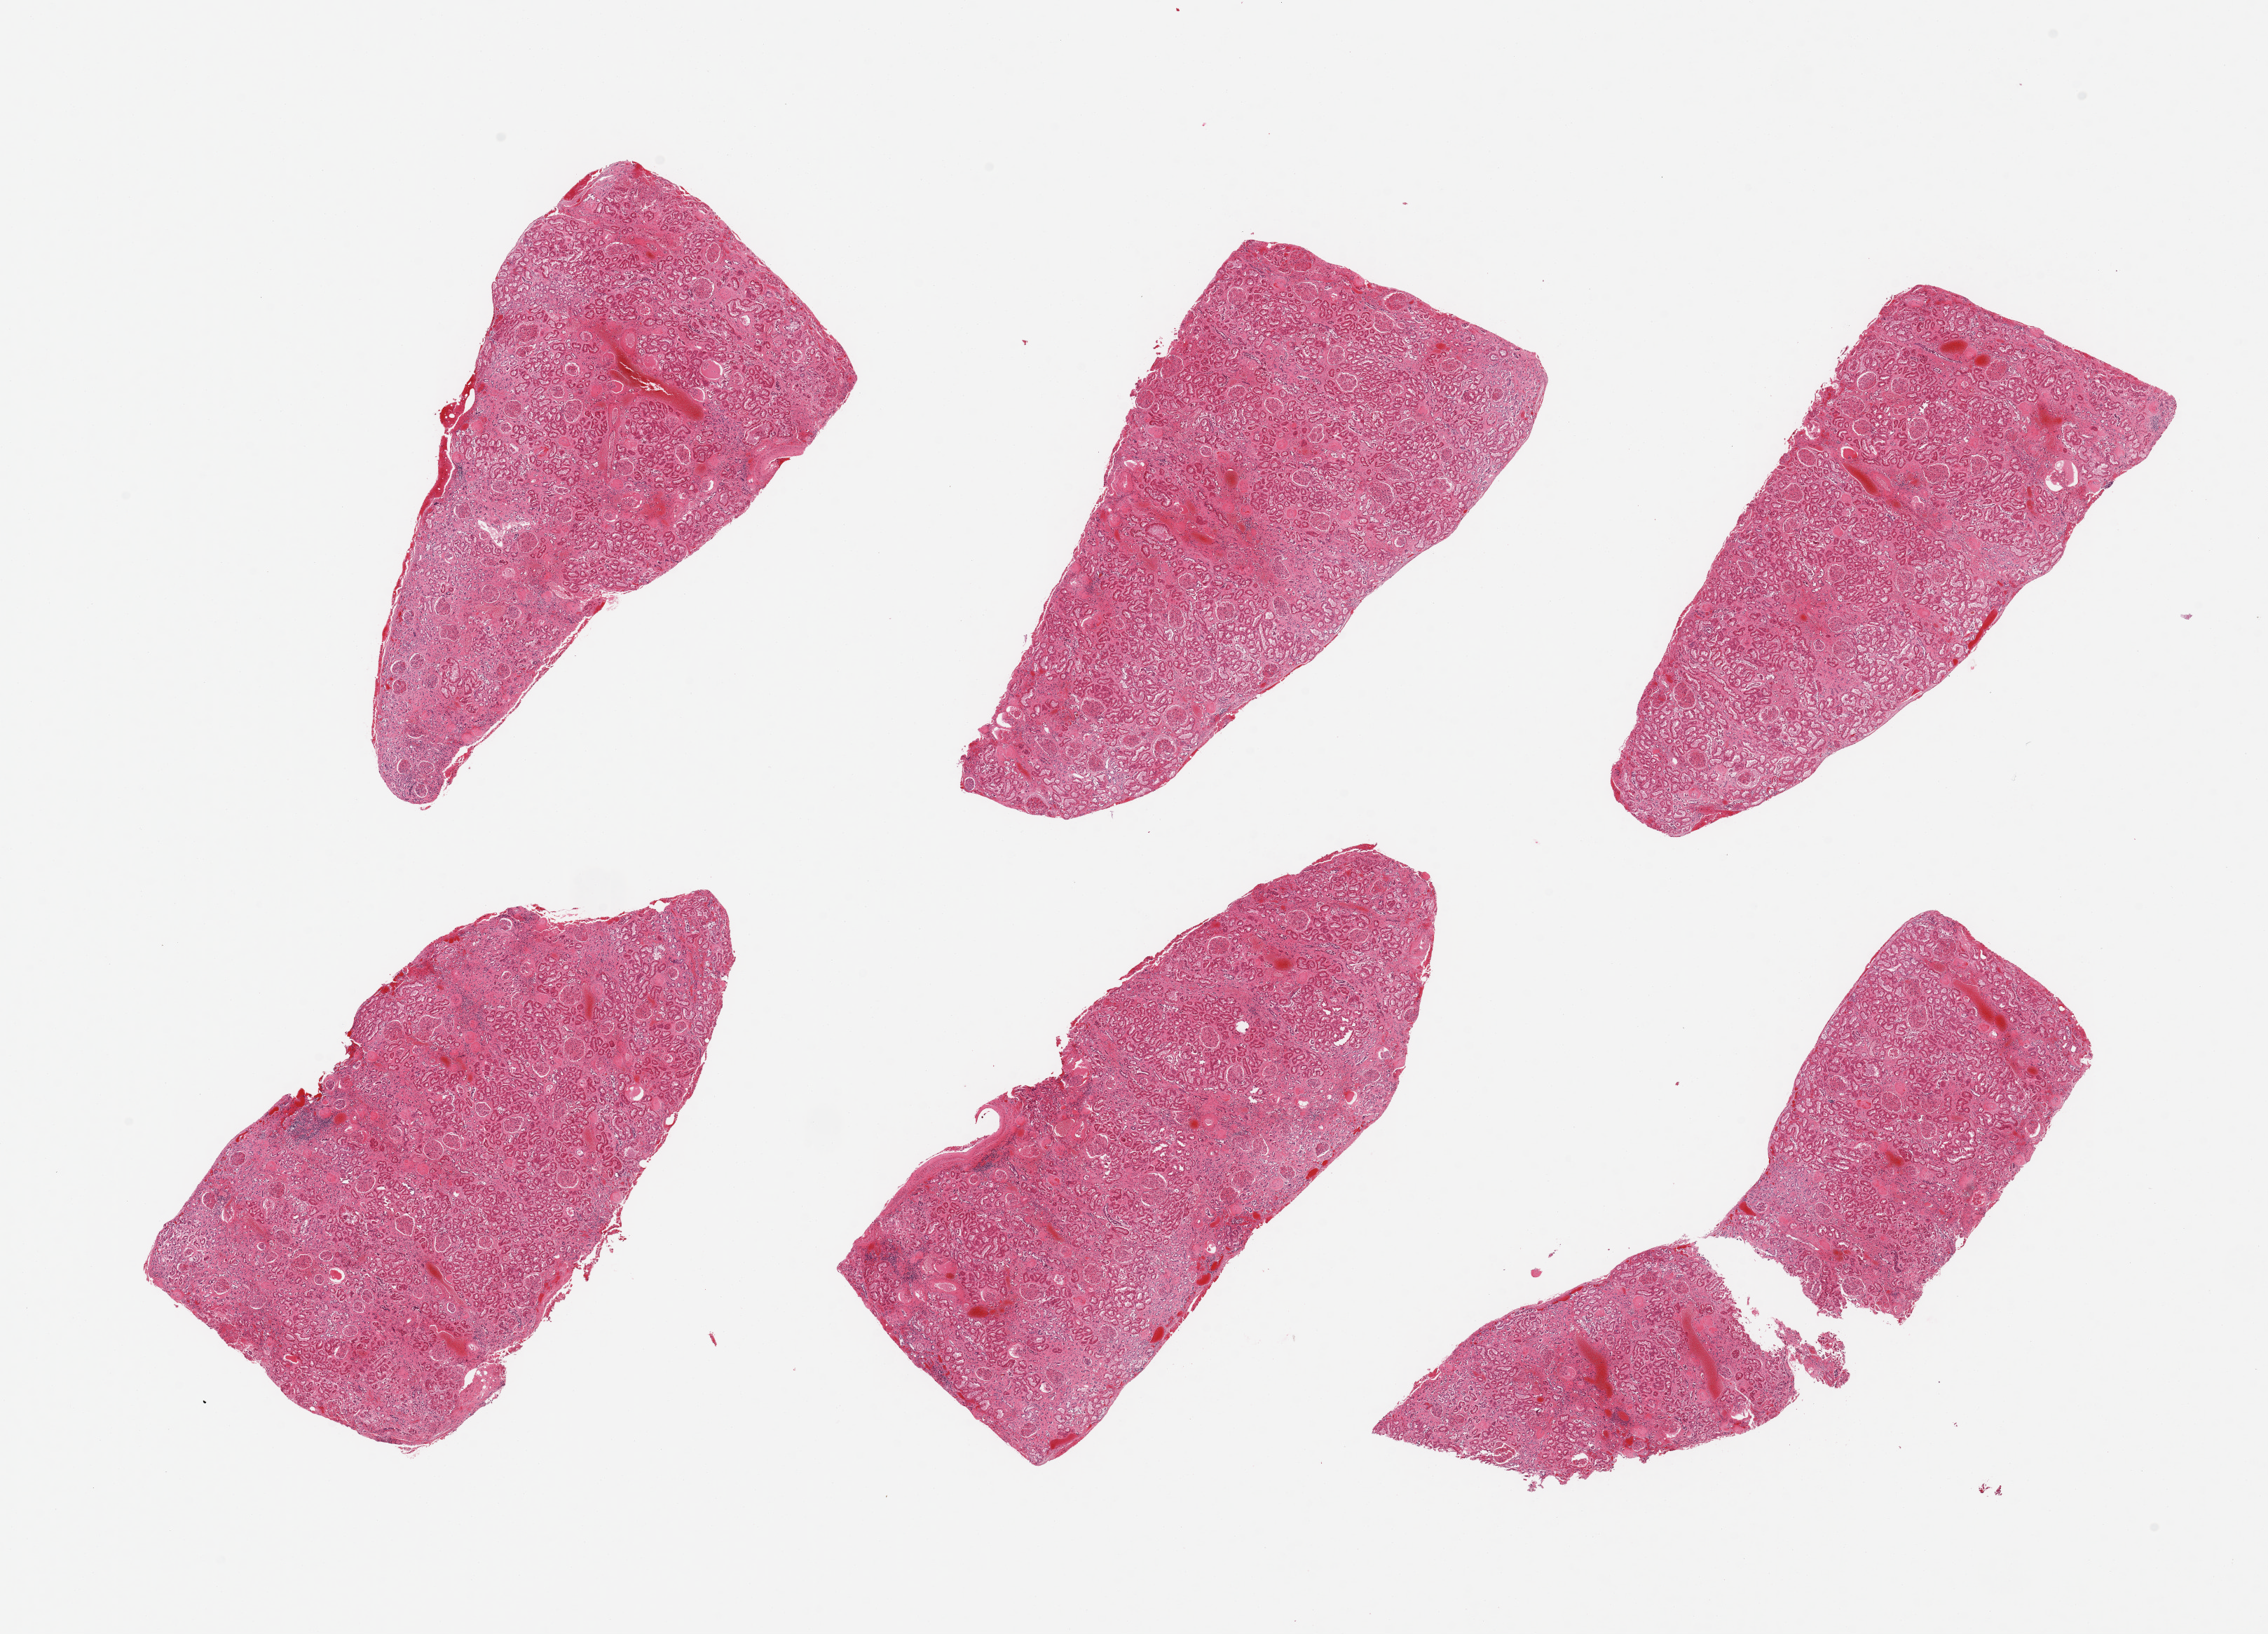
Whole-slide image, haematoxylin and eosin stain — low-resolution overview of the scanned area, about 25.6 x 18.4 mm (from a 20x scan), PAXgene-fixed paraffin-embedded (PFPE) section, sampled site (target tissue): renal cortex, tissue donor sample.
Review note (as recorded): 6 pieces; moderate interstitial scarring and vascular sclerosis; vascular congestion.